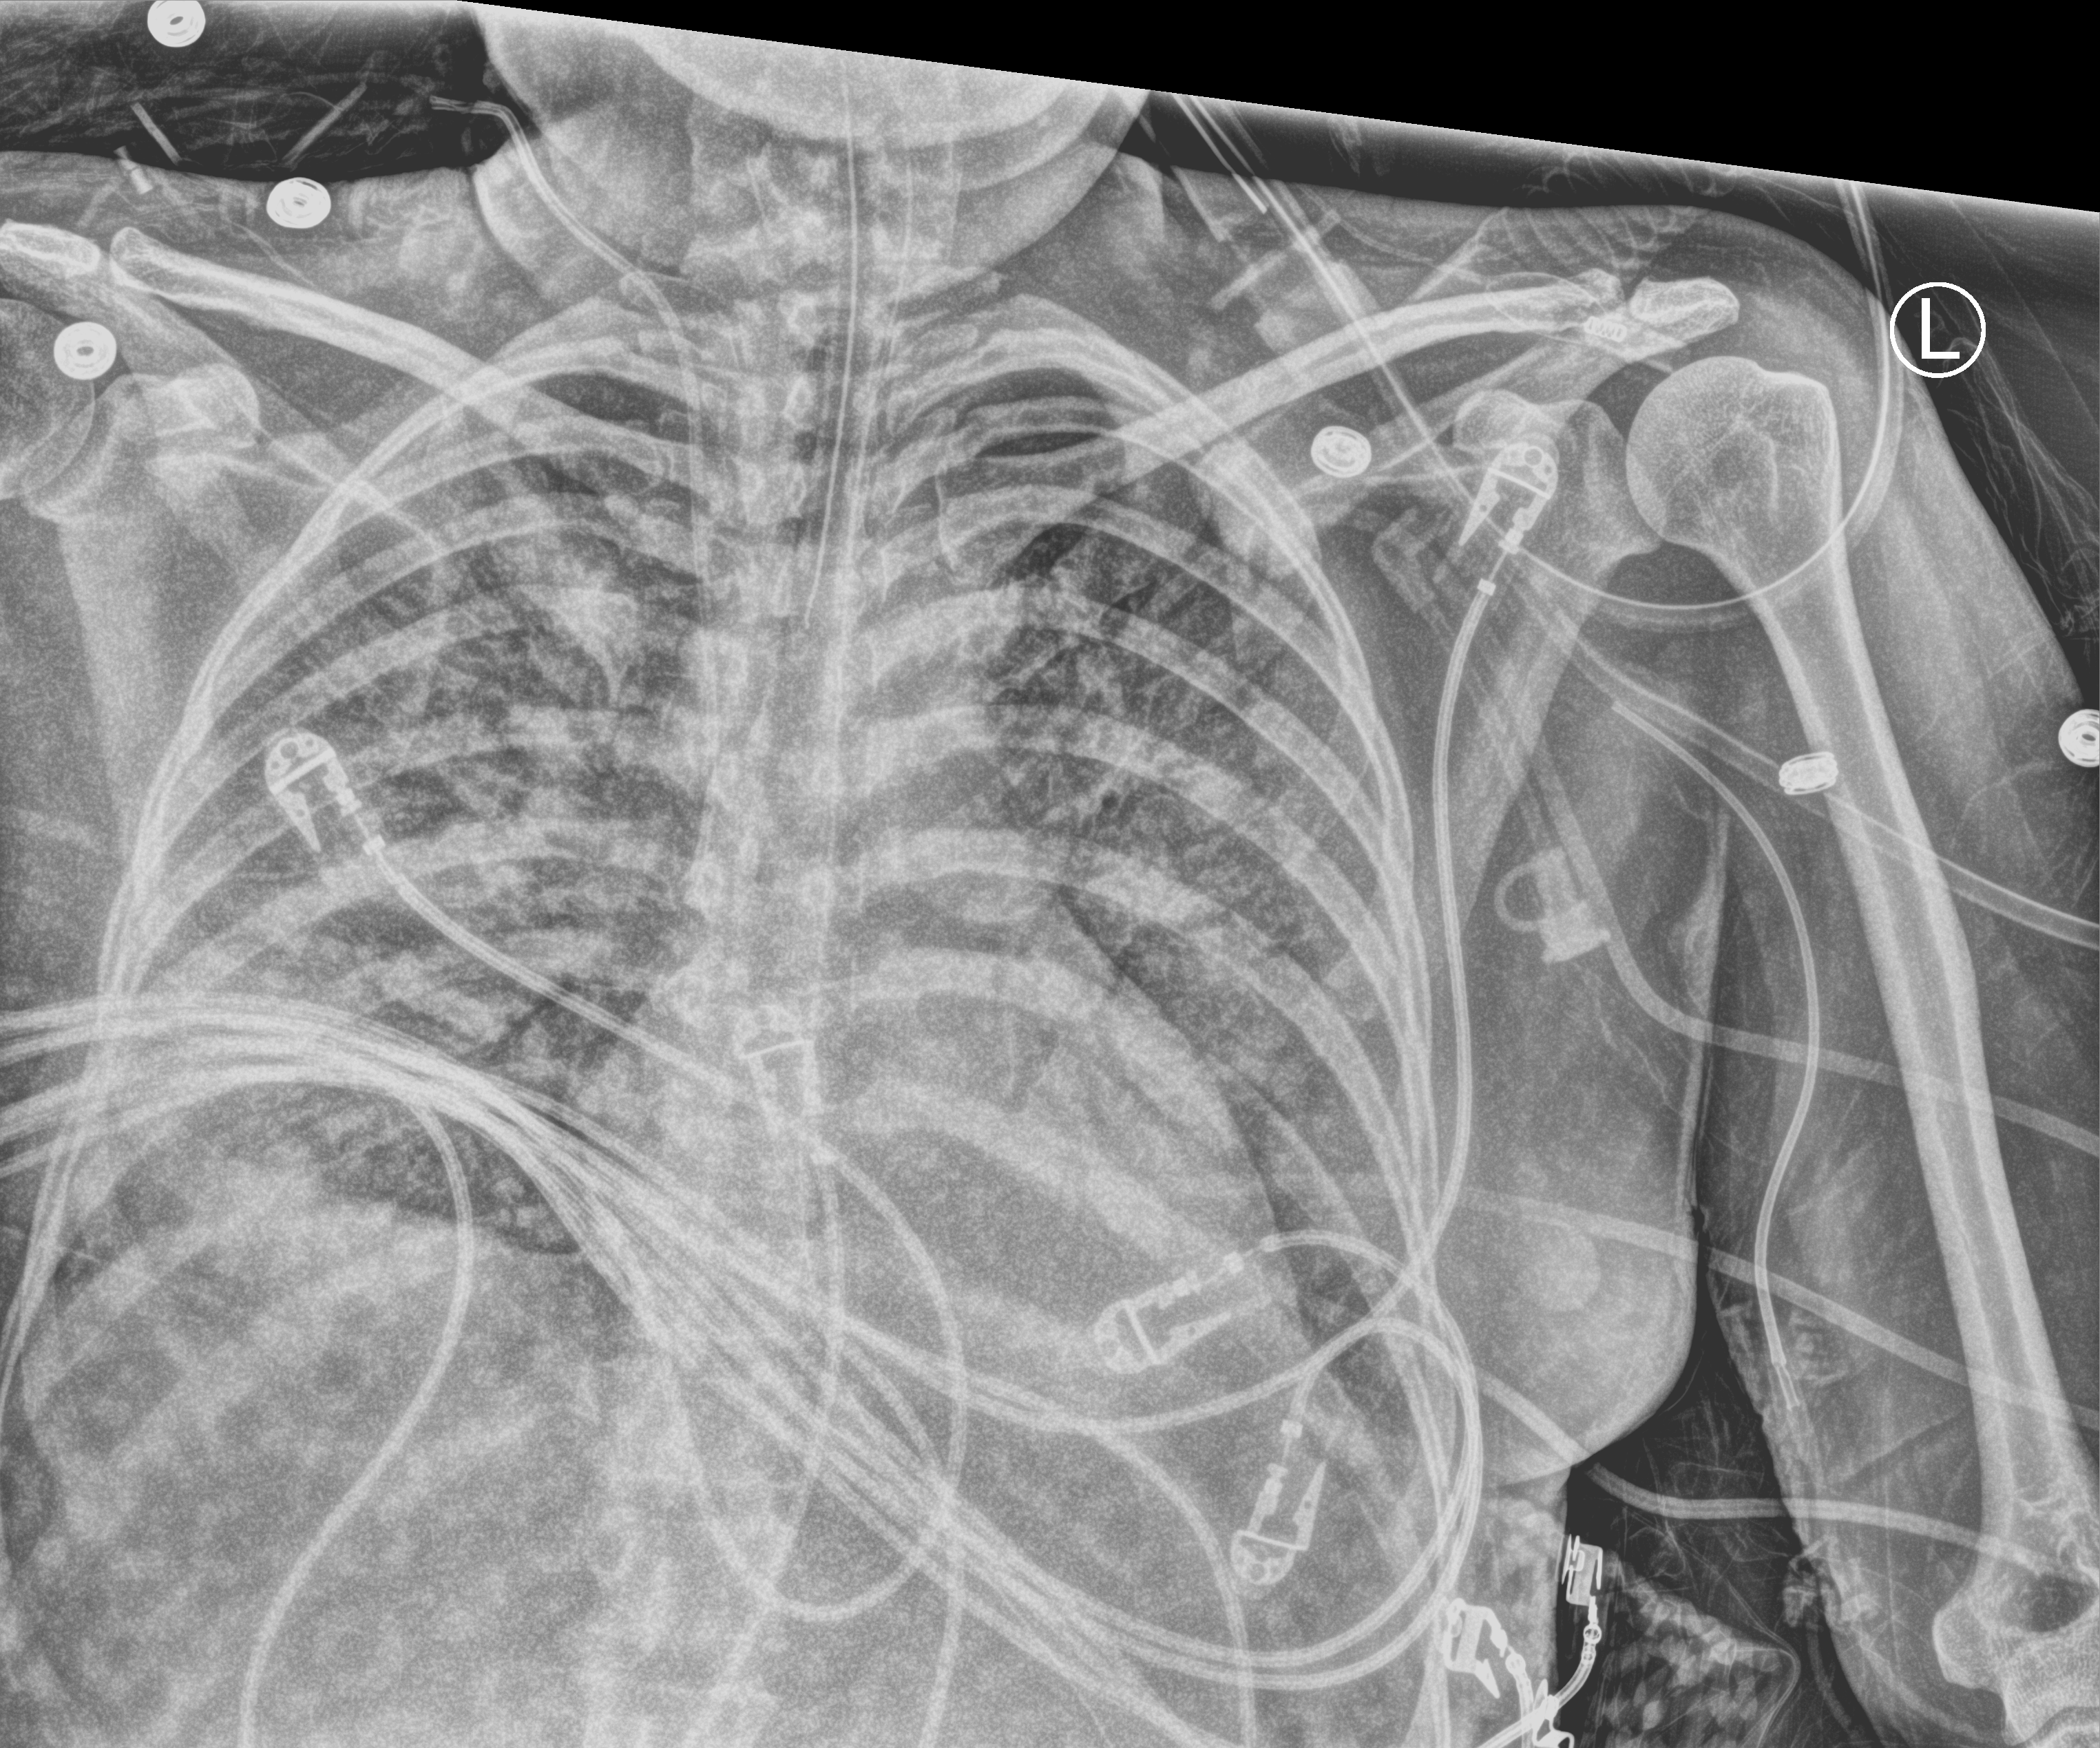
Portable chest radiograph. Female patient hospitalised with COVID-19, age 18–59 years.
From the hospital-stay record, not from the radiograph (when in the stay this image was taken is not recorded): hypertension (admission record): no.